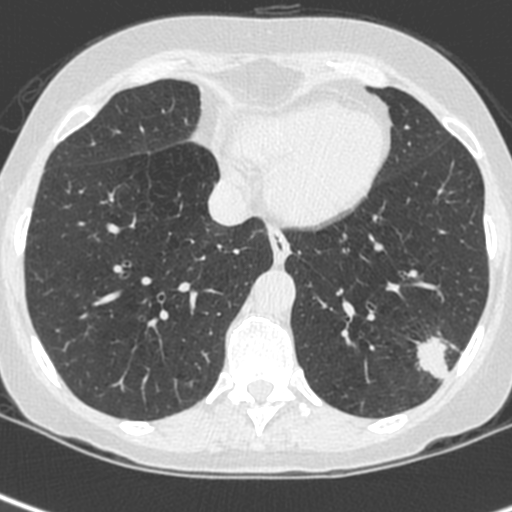
Chest CT (low-dose screening protocol), one axial image, first (baseline) screen, lung window (W 1500 / L -600 HU), 1.3 mm slice thickness, 120 kVp, slice 163 of 252 in the series, 512 × 512 image matrix, field of view 271 × 271 mm. Female, age 56 years at enrolment. Current smoker at enrolment.
Expert-annotated lung lesion, bounding box (x1, y1, x2, y2) in pixels: (410, 329, 472, 390). Screening reader's record for this exam (one nodule recorded; not confirmed to be the boxed lesion): non-calcified nodule or mass ≥4 mm, left lower lobe, 37 × 29 mm, spiculated (stellate) margins, ground glass attenuation. Later outcome: lung cancer diagnosed 91 days after this screen — squamous cell carcinoma, NOS, left lower lobe, poorly differentiated (G3), stage IIIA (AJCC 6th edition), 35 mm at pathology.